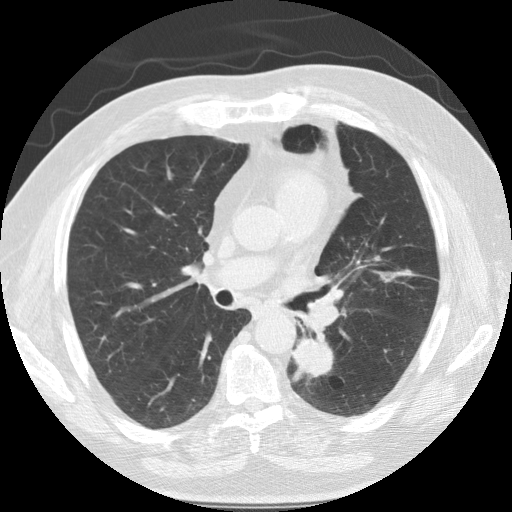
Low-dose screening chest CT, one axial slice. Reconstruction kernel STANDARD. Lung window (W 1500 / L -600 HU). 2.5 mm slice thickness. 512 × 512 image matrix, field of view 360 × 360 mm.
Annotated regions visible in this slice (manually delineated by an expert):
- lesion 1 (tumor, lower lobe of left lung): bounding box <292,333,334,382> (left, top, right, bottom; pixels)